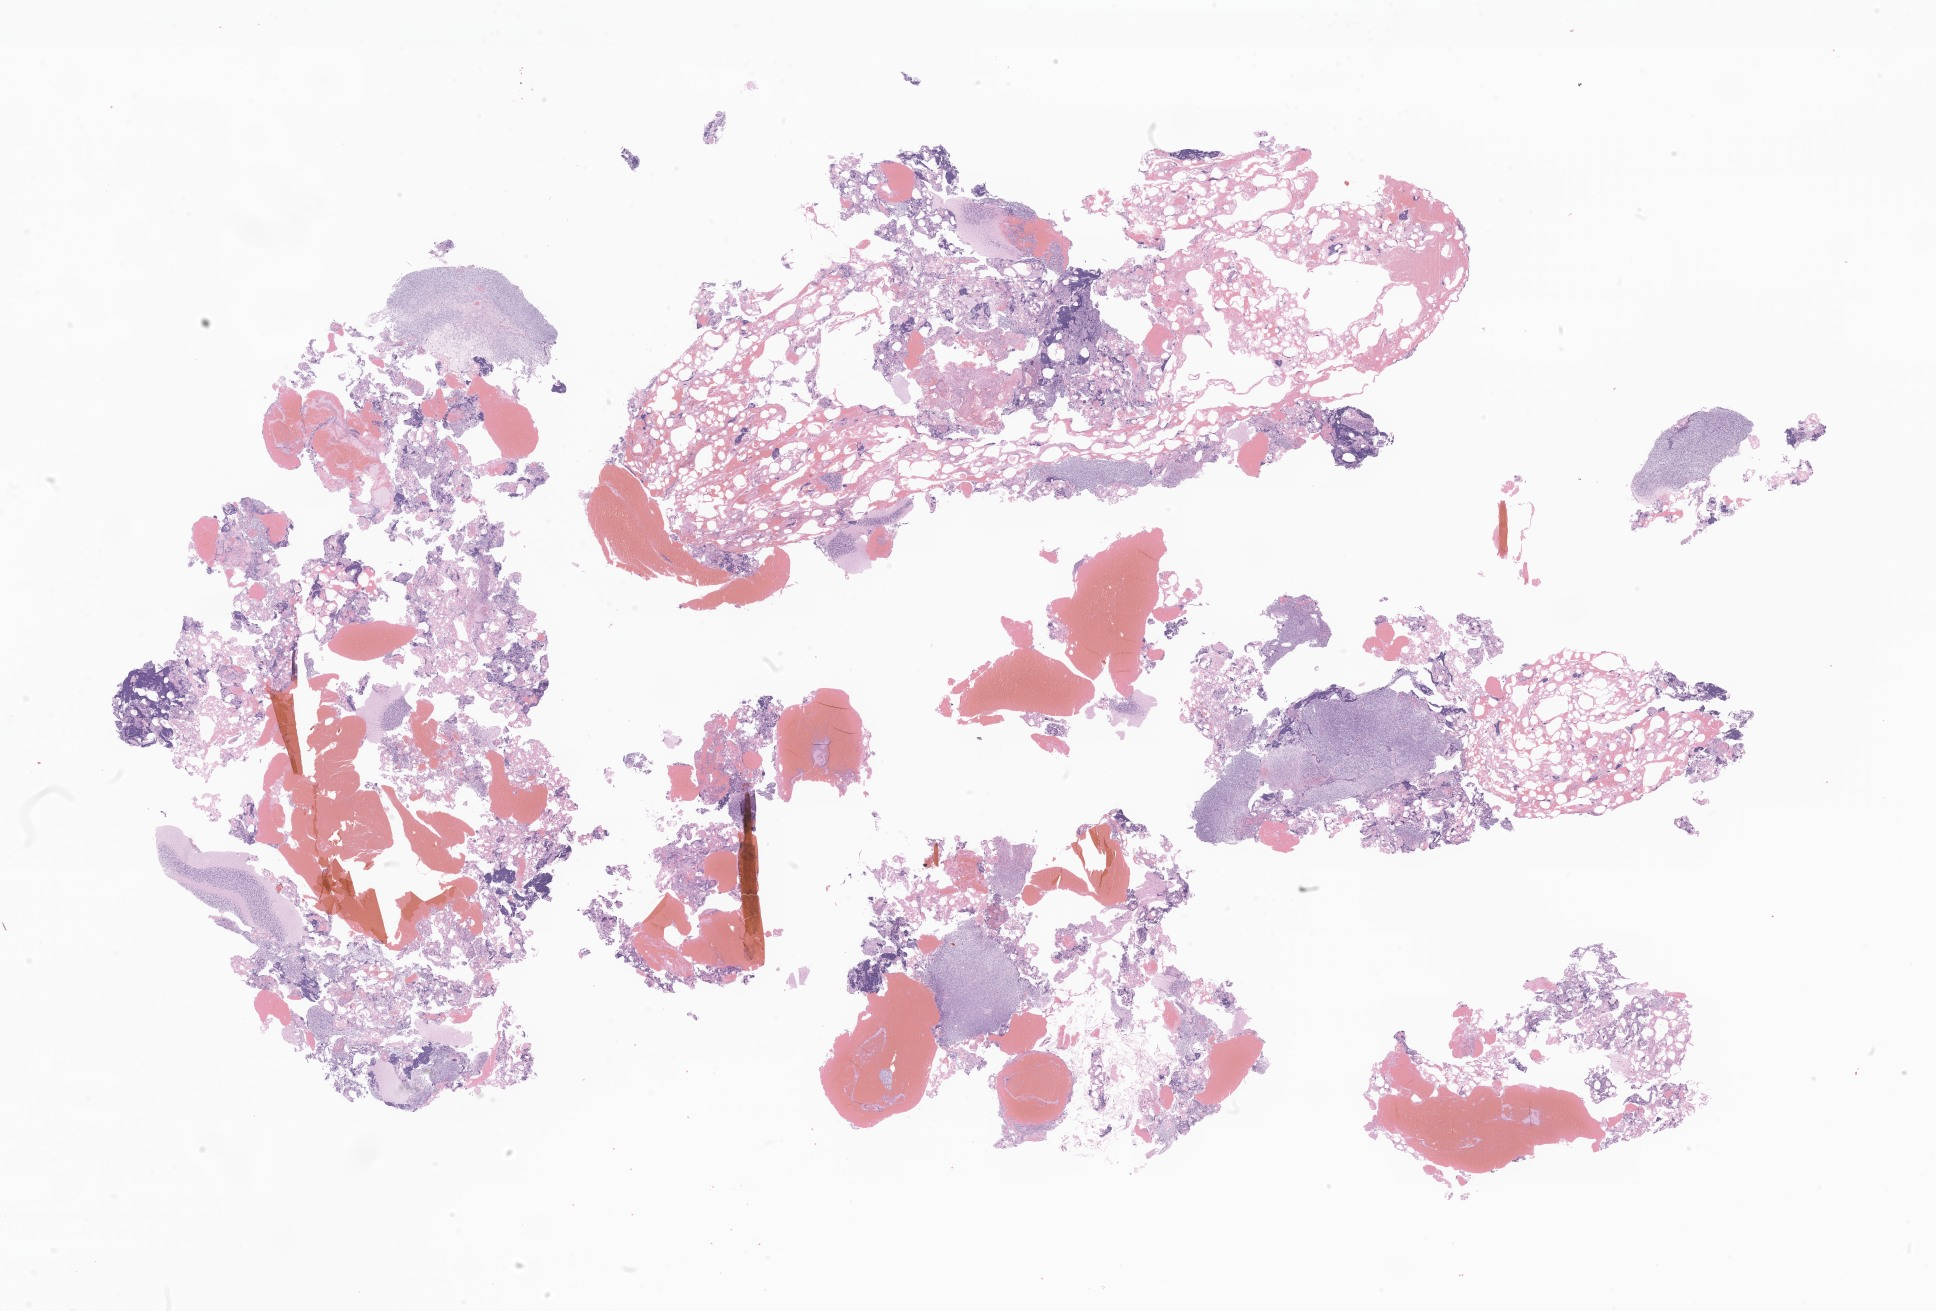
Hematoxylin and eosin (H&E) whole-slide image of tumor tissue from the brain — whole scanned area (about 32.6 x 22.1 mm) shown as a low-resolution overview; formalin-fixed paraffin-embedded section. Male patient, age 184 months (15 years 4 months).
• diagnosis: Medulloblastoma, NOS